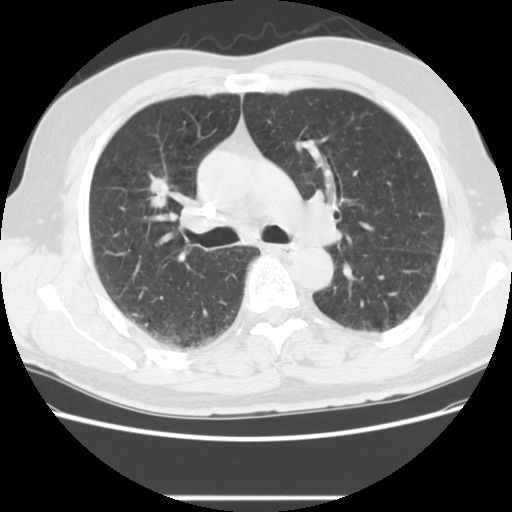
Axial slice from a low-dose chest CT screening exam; second screening round (one year after baseline); lung window (W 1500 / L -600 HU); 120 kVp; slice 55 of 139 in the series; 512 × 512 image matrix. Male participant, aged 59 years at enrolment. Current smoker at enrolment.
• Lesion marked by an expert reader, bounding box <137,173,178,216> (left, top, right, bottom; pixels).
• Screening reader's record for this exam (one nodule recorded; not confirmed to be the boxed lesion): non-calcified nodule or mass ≥4 mm, right upper lobe, 20 × 13 mm, spiculated (stellate) margins, soft tissue attenuation, pre-existing on the prior screen: yes; interval growth: yes.
• Later outcome: lung cancer diagnosed 267 days after this screen — large cell carcinoma, NOS, right upper lobe, poorly differentiated (G3), stage IIIA (AJCC 6th edition), 34 mm at pathology.